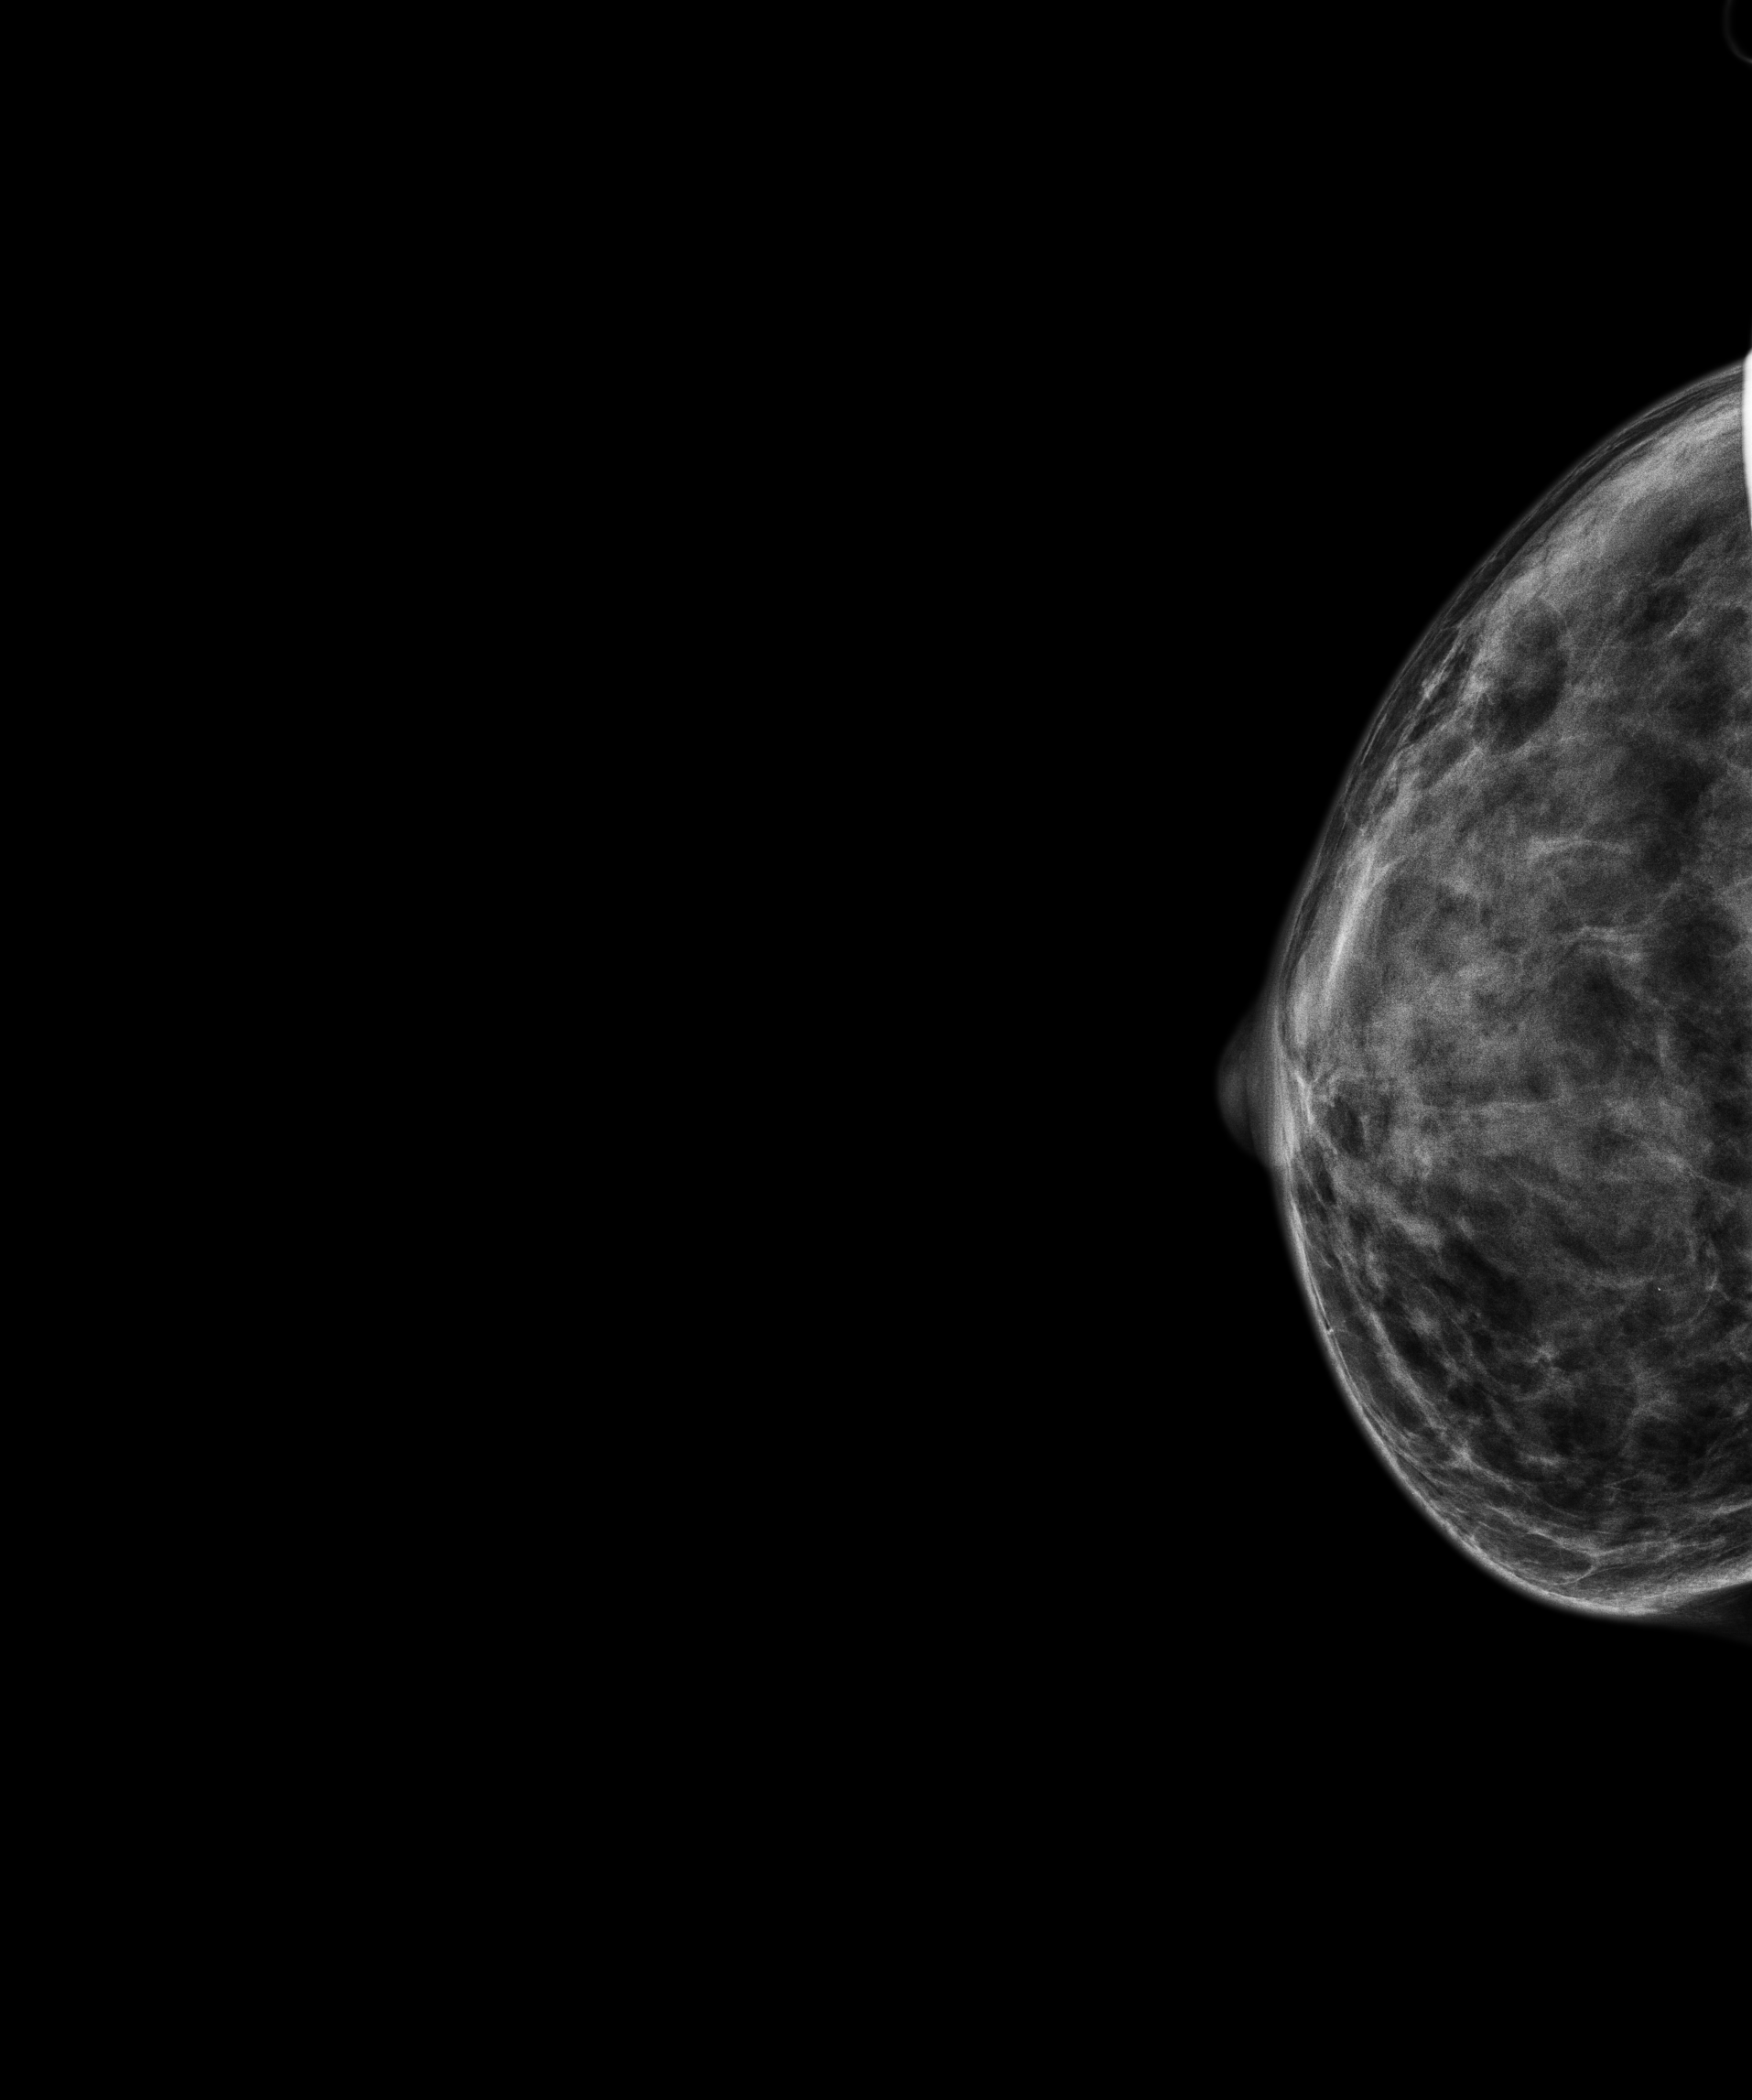
Full-field digital mammogram (FFDM), right breast, craniocaudal (CC) view, screening examination, compressed breast thickness 18.6 mm. Patient aged 54 years (female).
Final BI-RADS assessment for this screening round (tomosynthesis exam, both breasts): category 1.